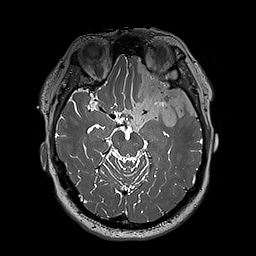
Brain MRI from a brain-tumour surgery series, one axial slice. Slice 130 of 192 in the series (ordered by position). 256 × 256 image matrix, field of view 250 × 250 mm. From the clinical record (not read from this slice): histopathology: Oligodendroglioma; WHO grade: 3; IDH mutation: yes; tumour location: Left Sylvian Fissure (Temporal).
Annotated regions visible in this slice (outlined manually by an expert reader):
- tumour: bounding box <124,60,197,131> (left, top, right, bottom; pixels)